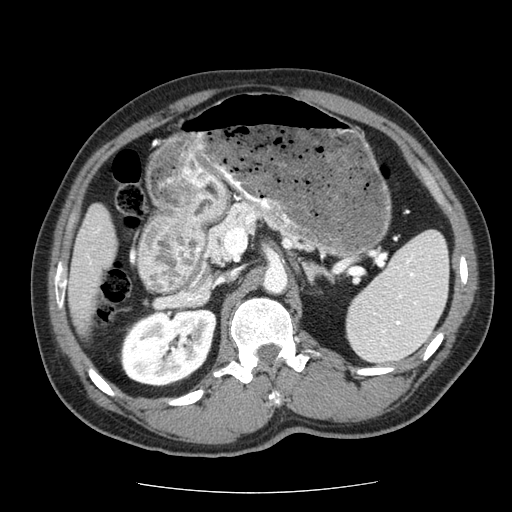
Contrast-enhanced abdominal CT (liver protocol), one axial slice; position 19 of 85 along the scan axis; reconstruction kernel STANDARD; 120 kVp; soft-tissue window (W 400 / L 40 HU); 2.5 mm slice thickness; 512 × 512 image matrix, field of view 360 × 360 mm. From the clinical record (not read from this slice): diagnosis: hepatocellular carcinoma (patient treated with transarterial chemoembolisation; whether this scan precedes or follows treatment is not stated here); TNM stage (as recorded): Stage-IIIA; Child-Pugh class: A; tumour nodularity: multinodular; tumour size: 8 cm.
Structures marked on this image (semi-automatically segmented with operator editing):
- liver parenchyma outside the tumour (the mass and vessels are separate outlines, so this box may not span the whole liver): bounding box <68,204,116,336> (left, top, right, bottom; pixels)
- liver vessels: <90,261,92,264>